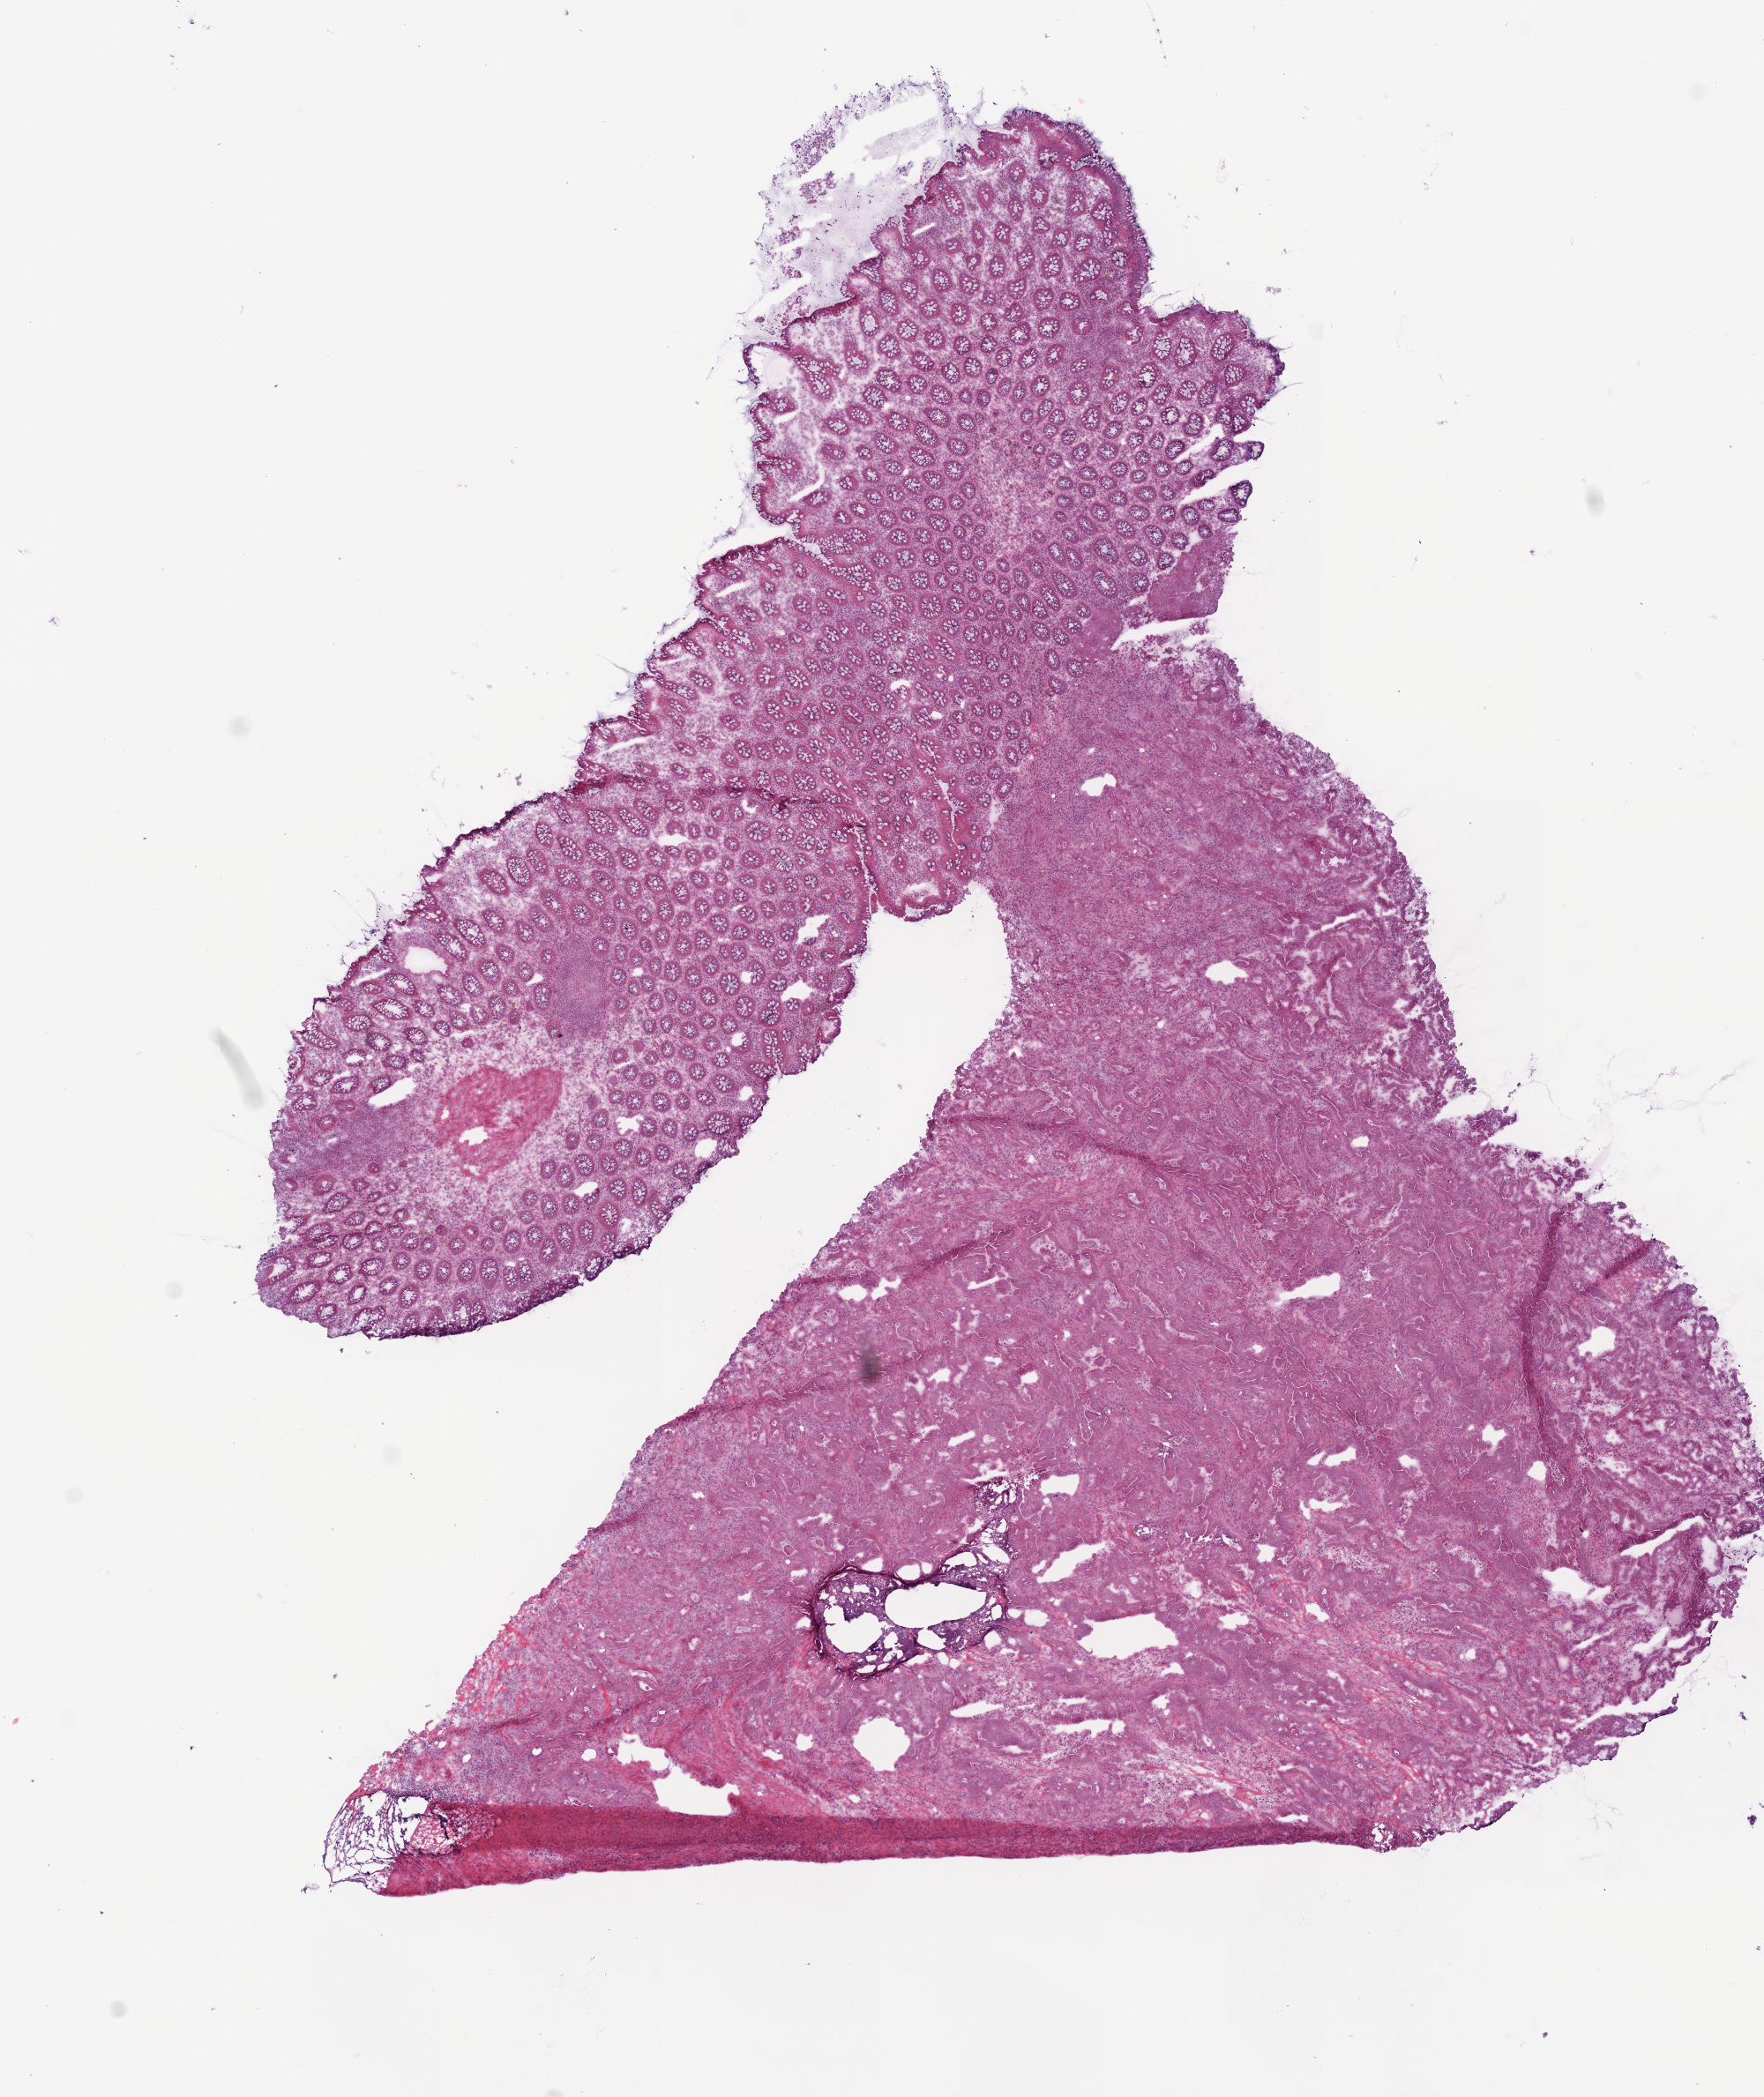
H&E whole-slide image — whole scanned area (about 8.0 x 9.5 mm) shown as a low-resolution overview, frozen section from the bottom of the tissue portion, primary tumour sample from the colon. Female patient; age at initial diagnosis 71 years. Slide review estimates, as recorded: tumour cells 50%, tumour nuclei 70%, normal cells 40%, stromal cells 5%, necrosis 5%.
* lymph nodes positive (case pathology): 5 of 23 examined
* diagnosis: Adenocarcinoma, NOS (ascending colon)
* AJCC pathologic stage: IV